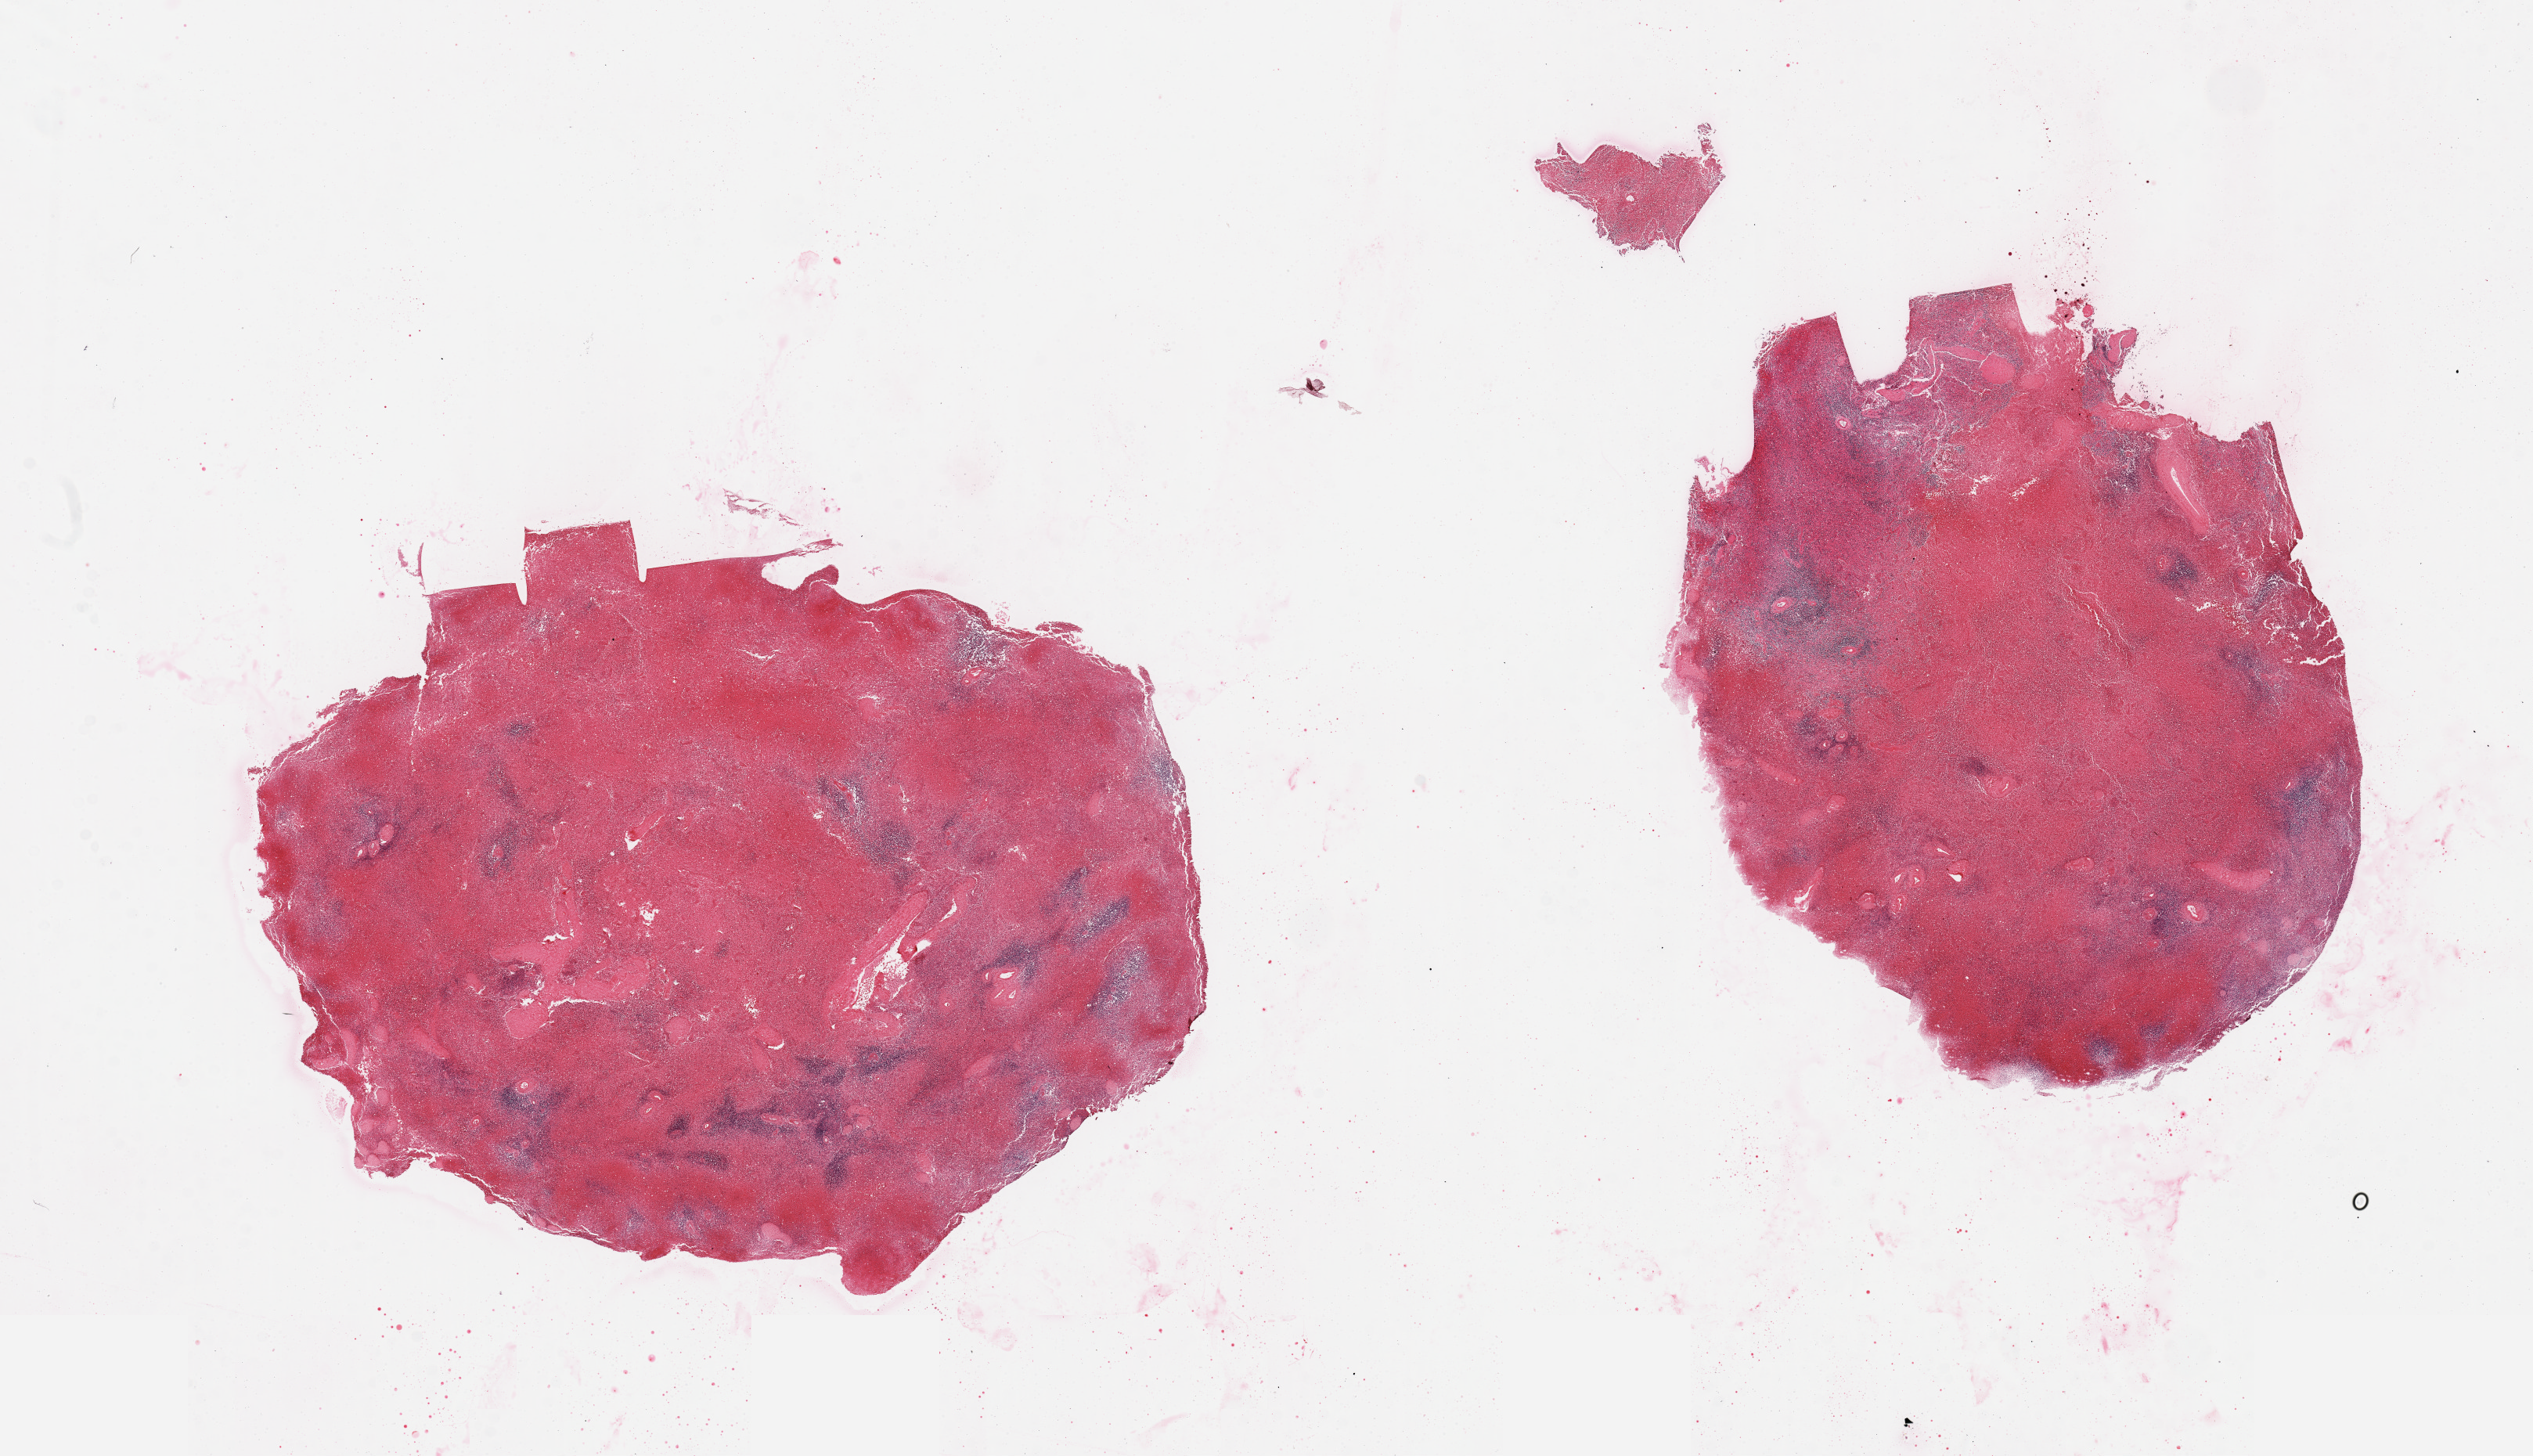
Haematoxylin and eosin whole-slide image, brightfield, low-resolution overview of the scanned area, about 25.6 x 14.7 mm. PAXgene-fixed paraffin-embedded (PFPE) section. Section of spleen (target tissue). Donor tissue sample. Female donor.
Reviewer comment on this tissue sample: 2 pieces, marked congestion, moderate-marked autolysis.